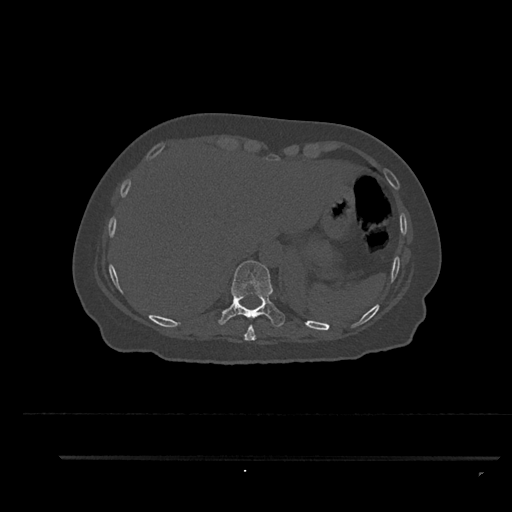
CT including the spine, one axial slice; position 370 of 797 along the scan axis; reconstruction kernel Br40s/3; bone window (W 1800 / L 400 HU); 512 × 512 image matrix. Female patient, age 44 years. From the clinical record (not read from this slice): primary cancer: renal; vertebrae with lytic lesions (as recorded): L1.
Annotated regions visible in this slice (semi-automatic segmentation, software-assisted and operator-edited):
- T10 vertebra: bounding box <218,260,285,327> (left, top, right, bottom; pixels)
- T9 vertebra: <244,325,256,341>